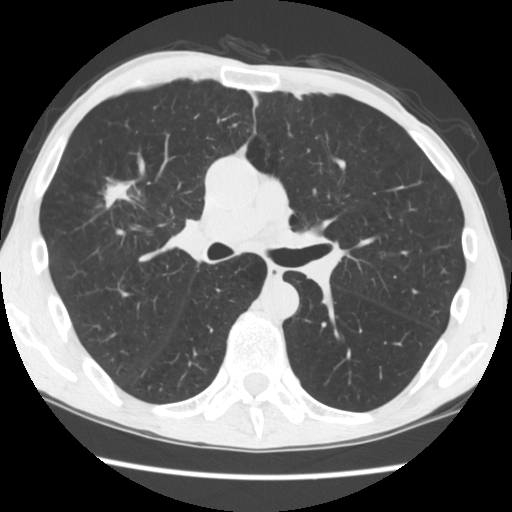
Low-dose screening chest CT, one axial slice; reconstruction kernel STANDARD; lung window (W 1500 / L -600 HU); 2.5 mm slice thickness; 512 × 512 image matrix, field of view 330 × 330 mm.
Structures marked on this image (expert manual segmentation):
- lesion 1 (tumor, upper lobe of right lung): bounding box <104,182,132,209> (left, top, right, bottom; pixels)